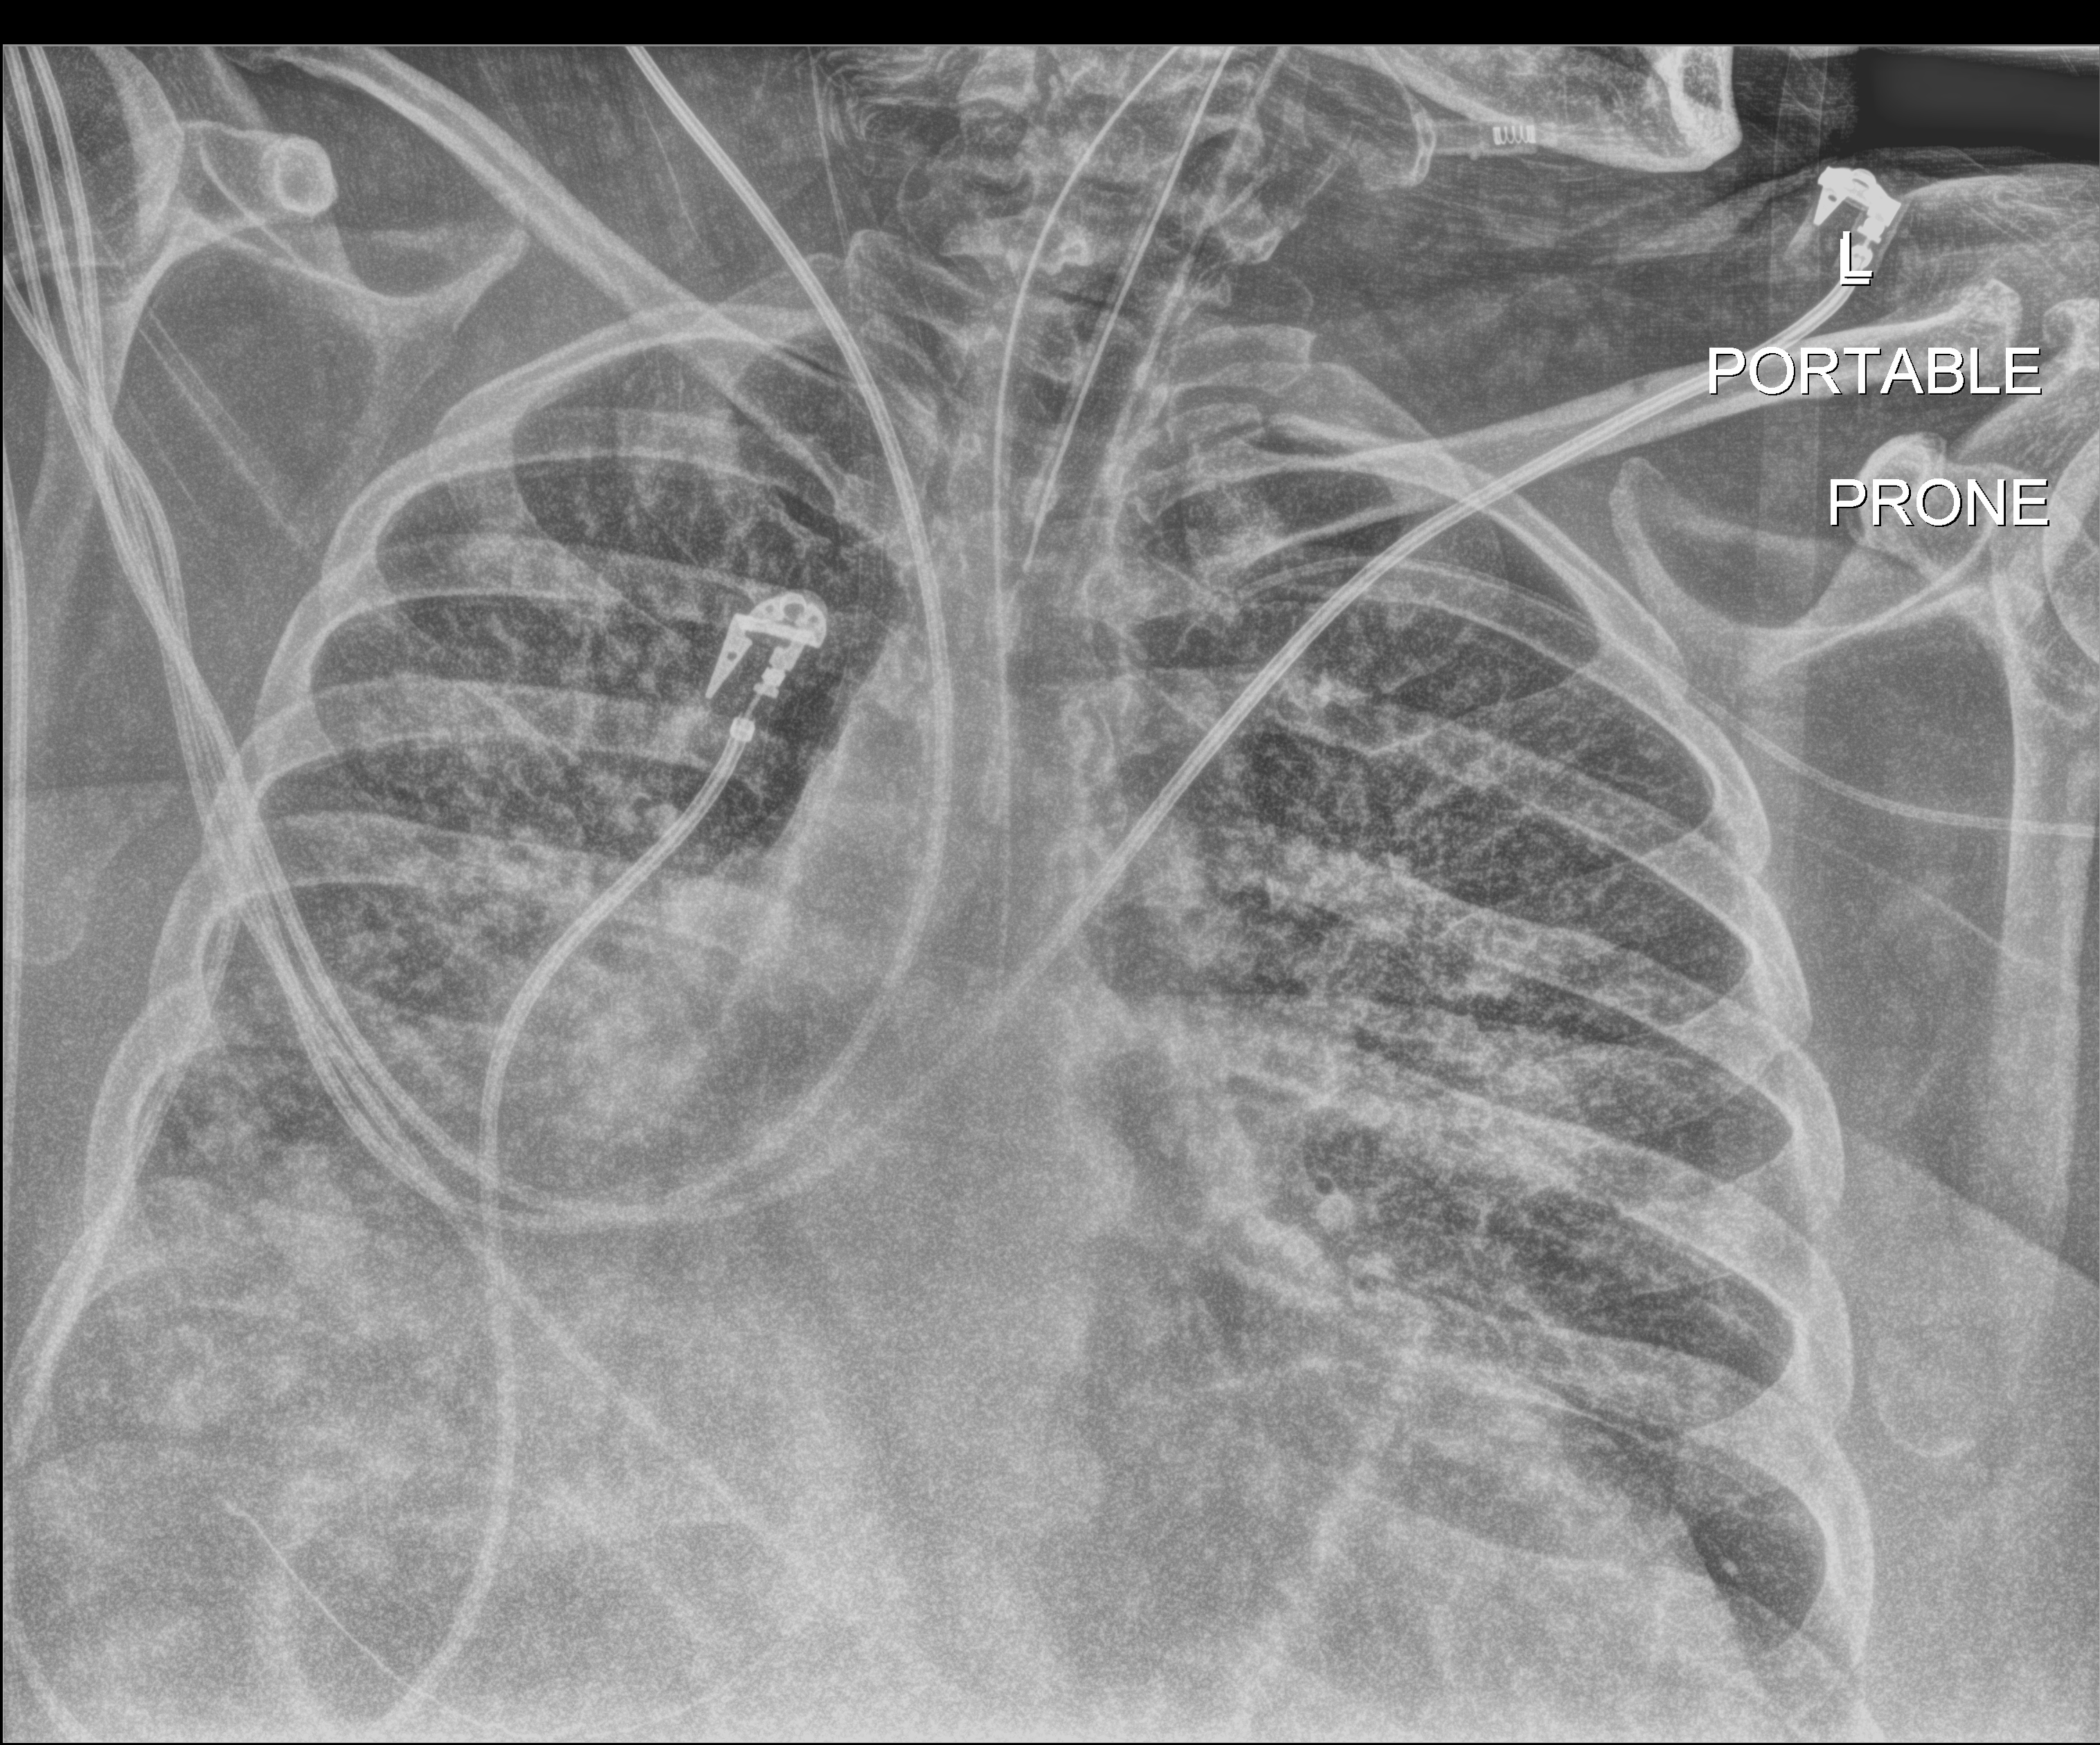
Chest X-ray, posteroanterior (PA) projection. Patient hospitalised with COVID-19, aged 18–59 years.
From the hospital-stay record, not from the radiograph (when in the stay this image was taken is not recorded): mechanically ventilated during this hospital stay: yes; admitted to intensive care during this hospital stay: yes.